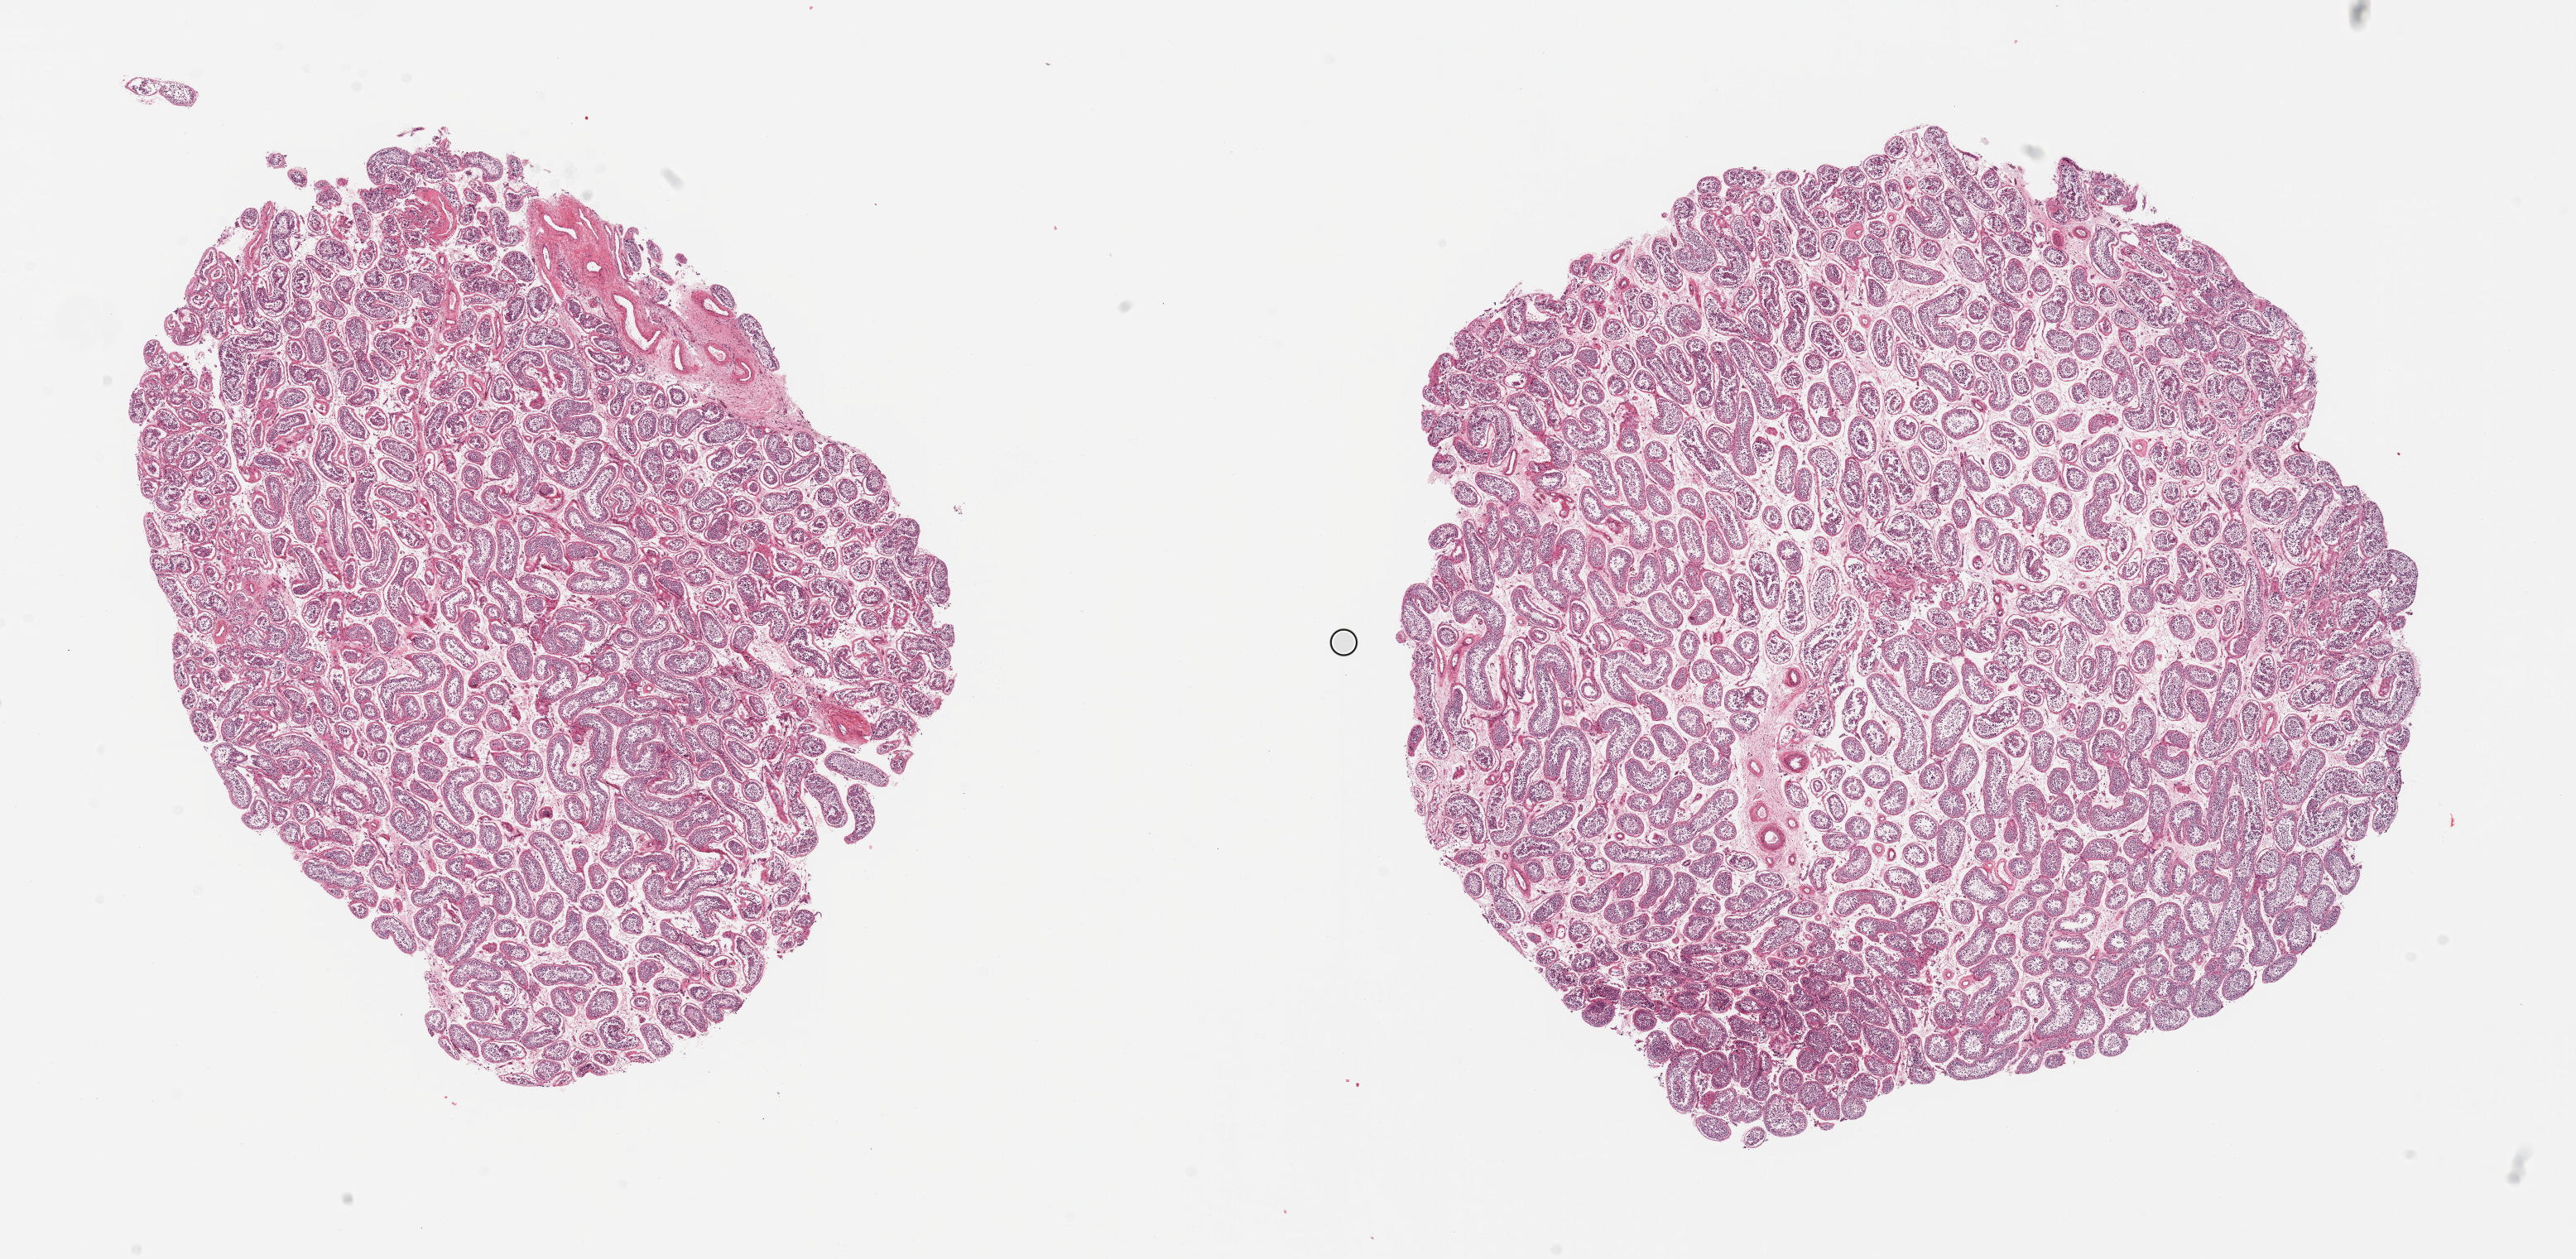
Digitized hematoxylin and eosin (H&E)-stained section — whole scanned area (about 24.6 x 12.0 mm) shown as a low-resolution overview. PAXgene-fixed, paraffin-embedded tissue. Section of testis (target tissue). Donor tissue sample. Male donor.
* reviewer comment on this tissue sample: 2 pieces, spermatogenesis appears reduced